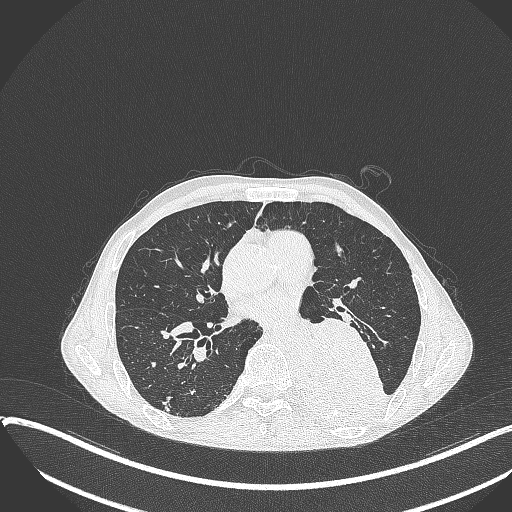
Chest CT, one axial slice. Reconstruction kernel B70f. 120 kVp. Lung window (W 1500 / L -600 HU). 512 × 512 image matrix. Patient: male, 57 years. Case-level facts recorded for this patient, not image findings: clinical TNM (as recorded): T4 N0 M0.
Annotated regions visible in this slice (bounding box drawn by a radiologist):
- lung tumour (recorded histology: squamous cell carcinoma): bounding box [x1, y1, x2, y2] px = [293, 314, 391, 430]